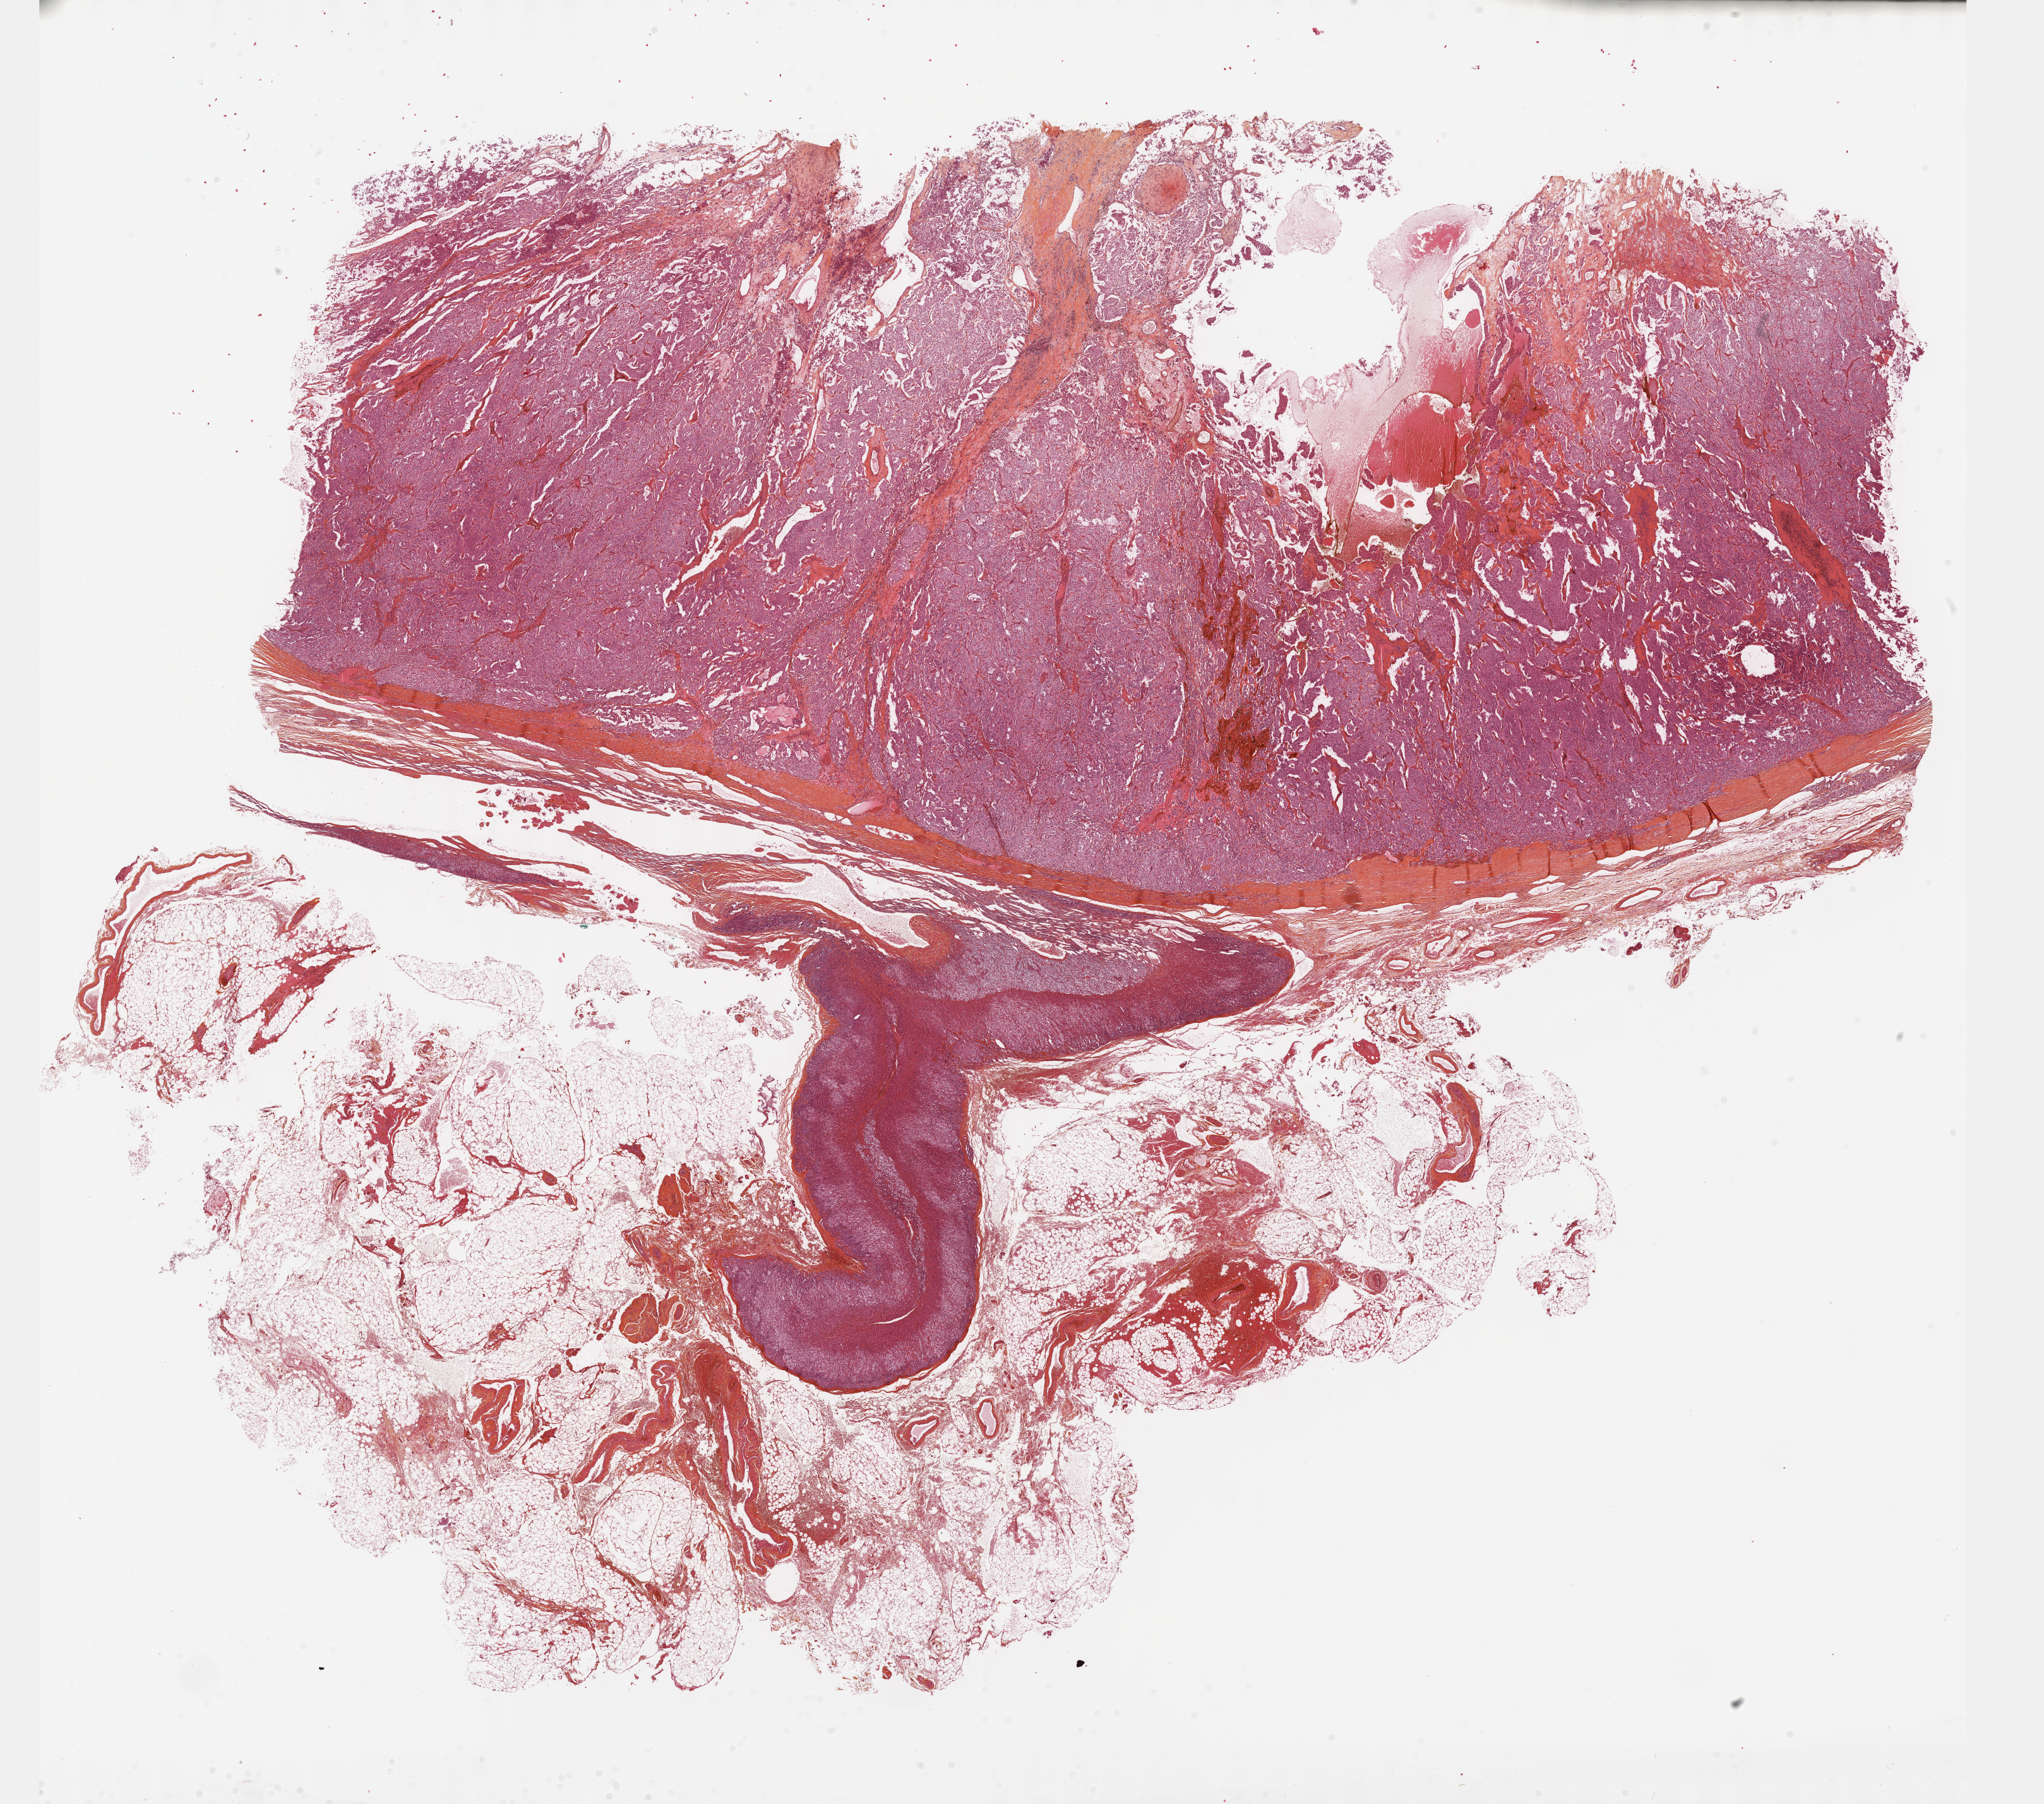
Whole-slide histology image, H&E-stained, a low-resolution overview of the entire scanned area, about 26.2 x 23.1 mm, formalin-fixed paraffin-embedded (FFPE) diagnostic section, primary tumour sample from the adrenal gland. Male, age 23 years at initial diagnosis.
Laterality: left. Pathologic diagnosis: Pheochromocytoma, malignant.